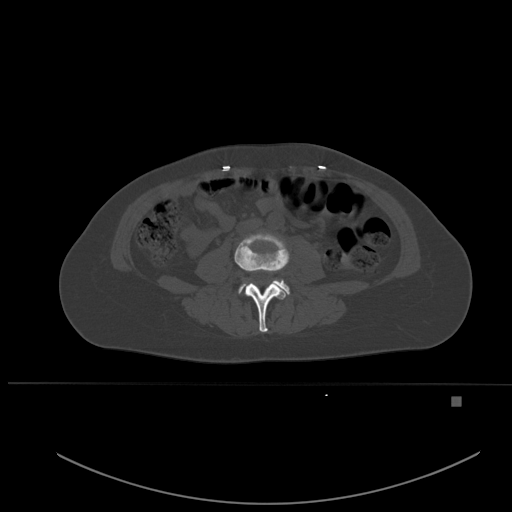
CT including the spine, one axial slice; bone window (W 1800 / L 400 HU); 1.5 mm slice thickness; 512 × 512 image matrix, field of view 443 × 443 mm. Patient: female, 49 years. From the clinical record (not read from this slice): primary cancer: breast; vertebrae with lytic lesions (as recorded): L3, T12, L4.
Structures marked on this image (semi-automatic segmentation, software-assisted and operator-edited):
- L3 vertebra: bounding box <234,233,290,332> (left, top, right, bottom; pixels)
- L4 vertebra: <238,279,290,295>